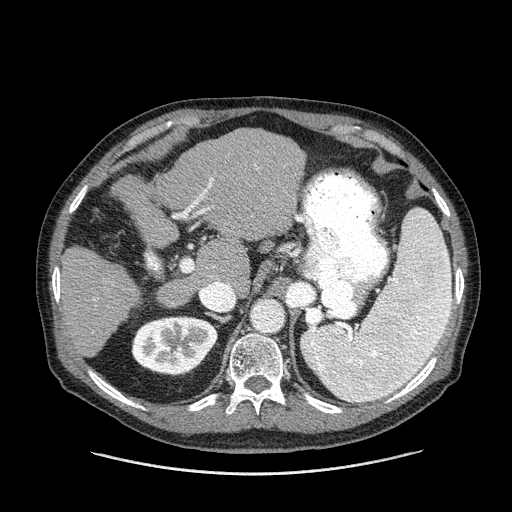
Contrast-enhanced abdominal CT (liver protocol), one axial slice; position 88 of 180 along the scan axis; reconstruction kernel STANDARD; 120 kVp; one of 2 acquisitions stored at this slice position; soft-tissue window (W 400 / L 40 HU); 512 × 512 image matrix, field of view 420 × 420 mm. Case-level facts recorded for this patient, not image findings: diagnosis: hepatocellular carcinoma (patient treated with transarterial chemoembolisation; whether this scan precedes or follows treatment is not stated here); TNM stage (as recorded): Stage-II; Child-Pugh class: A.
Outlined on this slice (semi-automatically segmented with operator editing):
- liver parenchyma outside the tumour (the mass and vessels are separate outlines, so this box may not span the whole liver): bounding box <58,128,304,356> (left, top, right, bottom; pixels)
- liver vessels: <185,164,256,214>